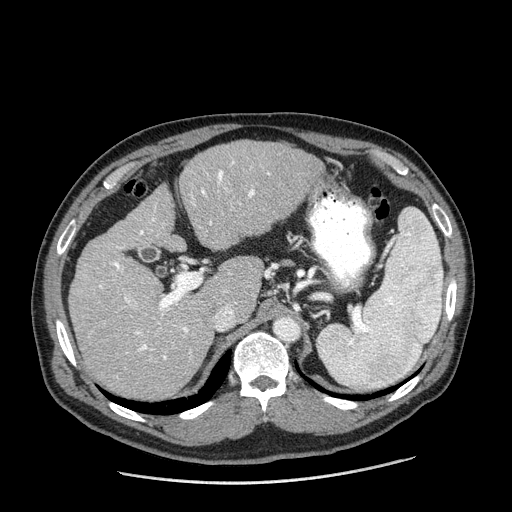
Contrast-enhanced abdominal CT (liver protocol), one axial slice; slice 119 of 198 in the series (ordered by position); one of 2 acquisitions stored at this slice position; soft-tissue window (W 400 / L 40 HU); 2.5 mm slice thickness; 512 × 512 image matrix, field of view 400 × 400 mm. From the clinical record (not read from this slice): diagnosis: hepatocellular carcinoma (patient treated with transarterial chemoembolisation; whether this scan precedes or follows treatment is not stated here); TNM stage (as recorded): Stage-II; Child-Pugh class: A; tumour nodularity: multinodular; tumour size: 2.6 cm.
Annotated regions visible in this slice (semi-automatically segmented with operator editing):
- liver parenchyma outside the tumour (the mass and vessels are separate outlines, so this box may not span the whole liver): bounding box (x1, y1, x2, y2) in pixels: (68, 140, 324, 398)
- liver vessels: (99, 162, 270, 360)